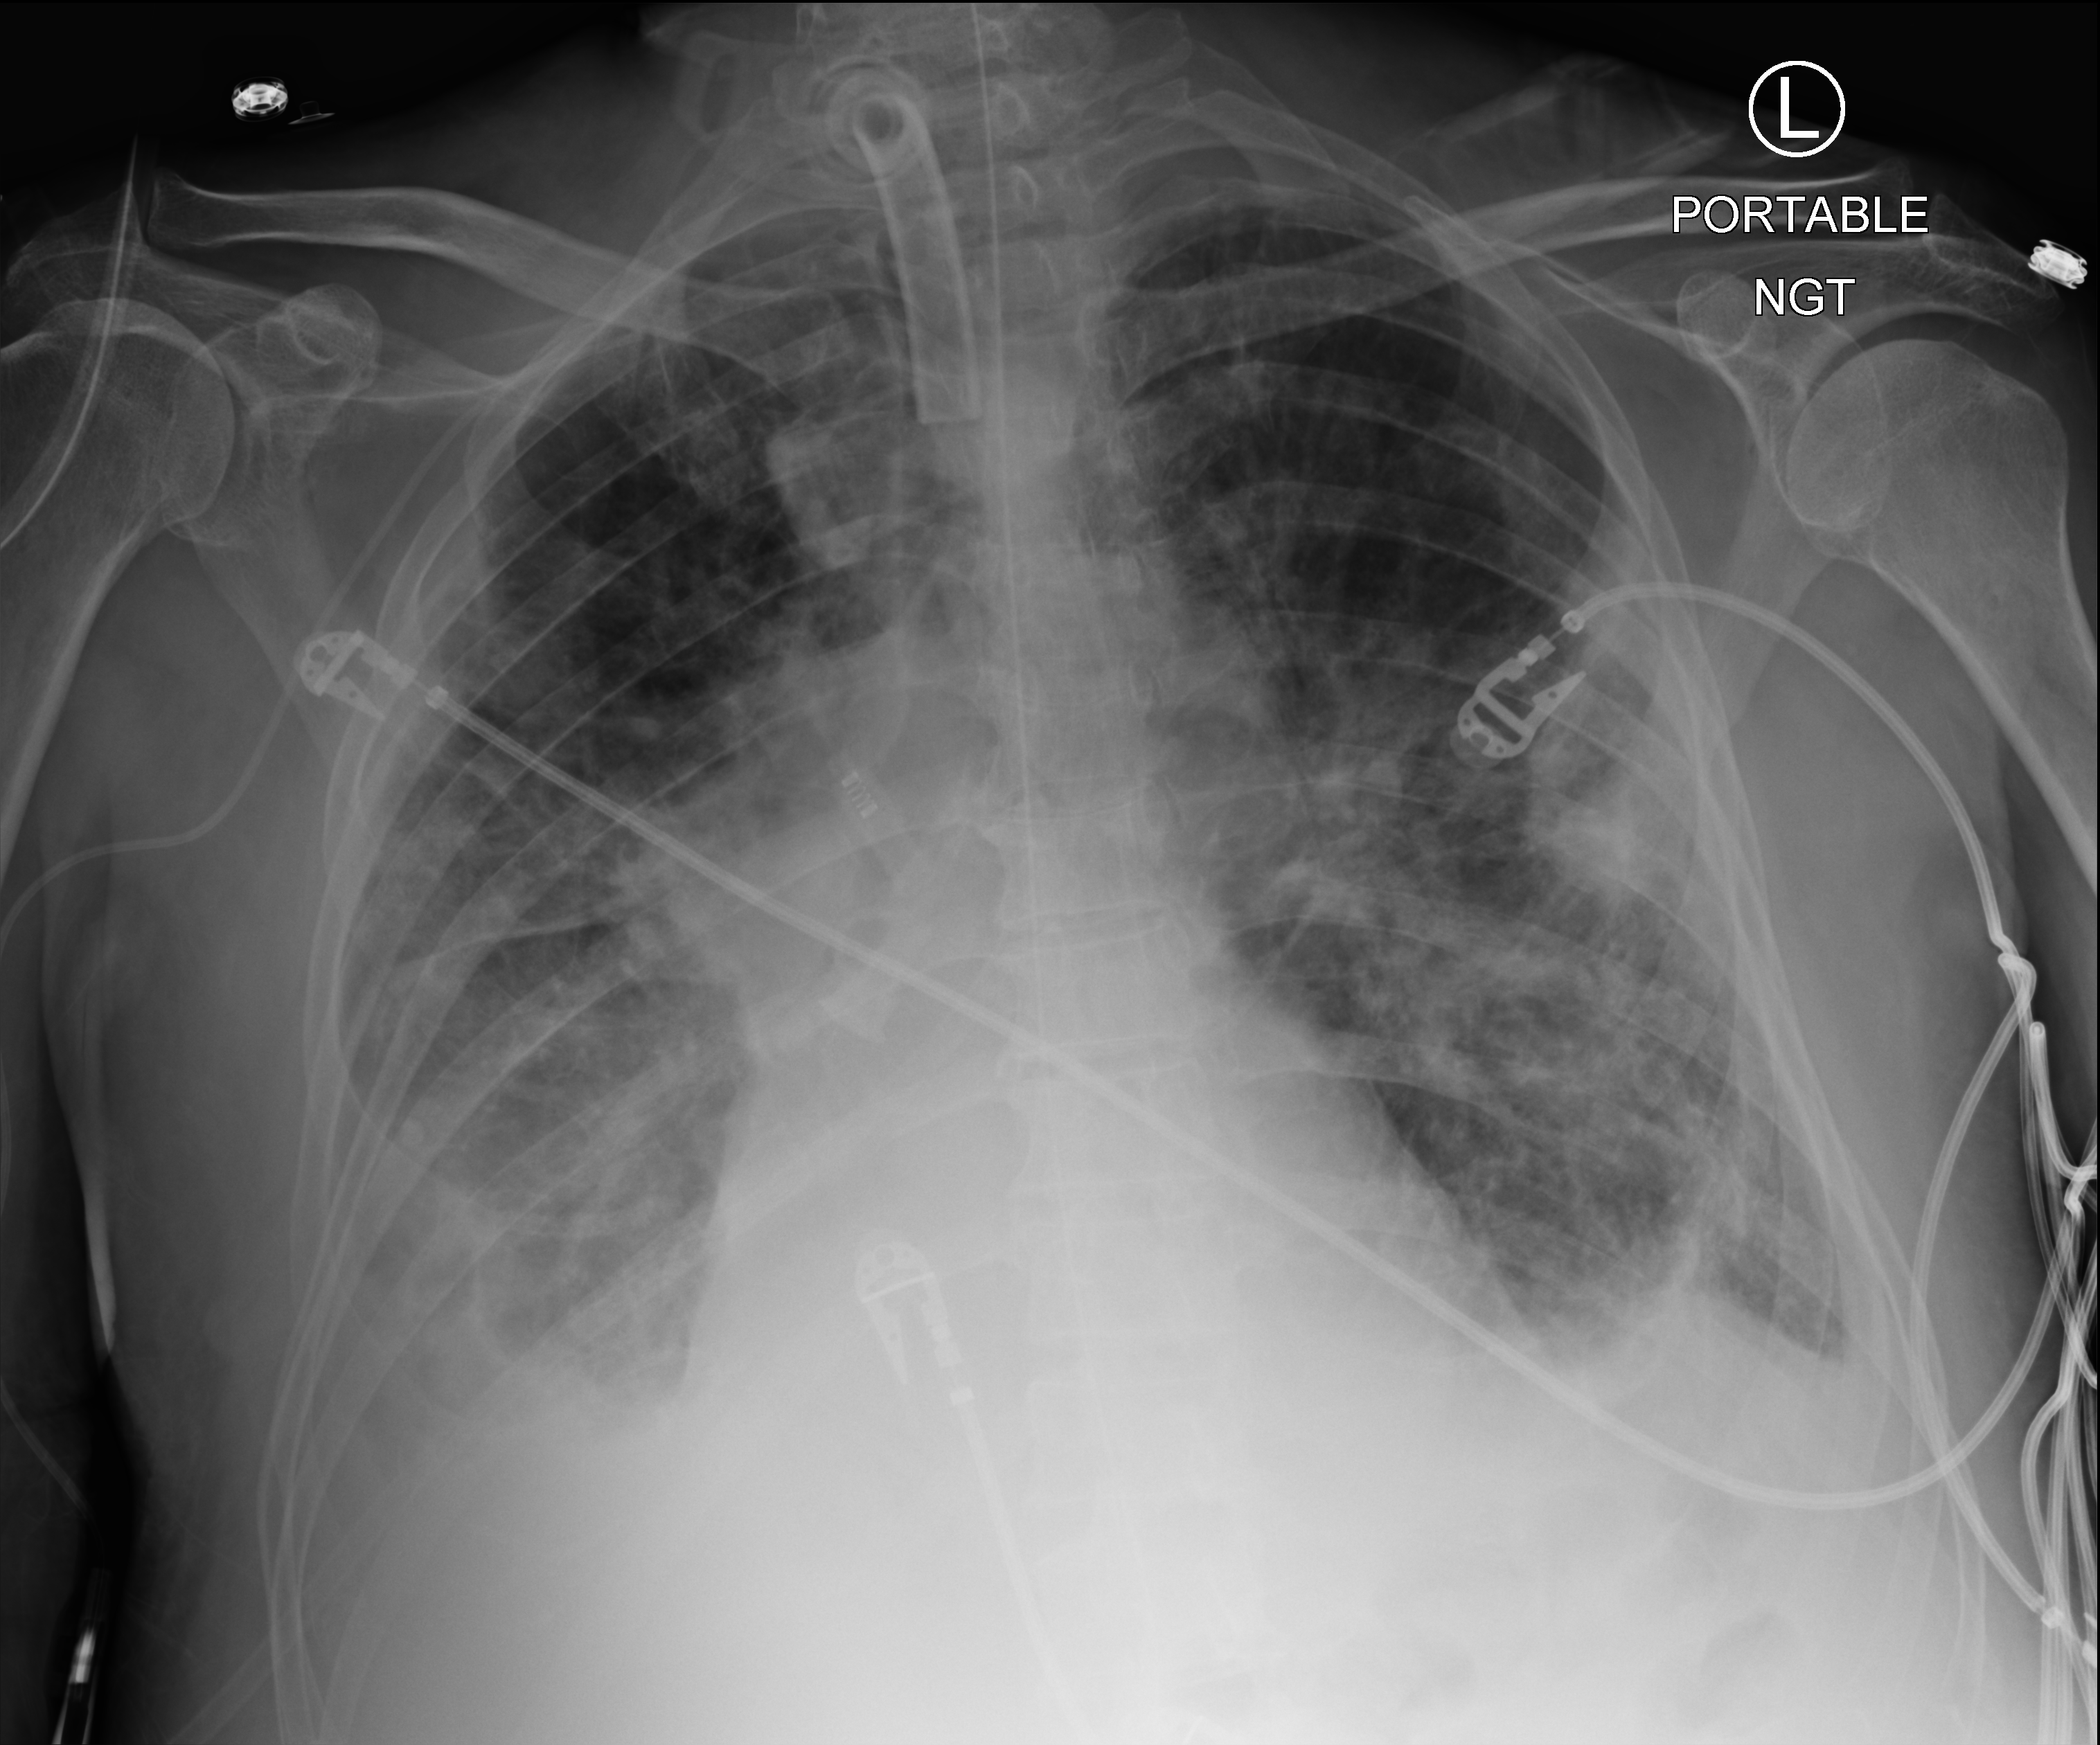
Bedside chest radiograph (computed radiography); anteroposterior (AP) projection. Male patient hospitalised with COVID-19, age 75–90 years.
Admission-level facts for this patient (not findings on this image; timing relative to this image not recorded): mechanically ventilated during this hospital stay: yes; admitted to intensive care during this hospital stay: yes.